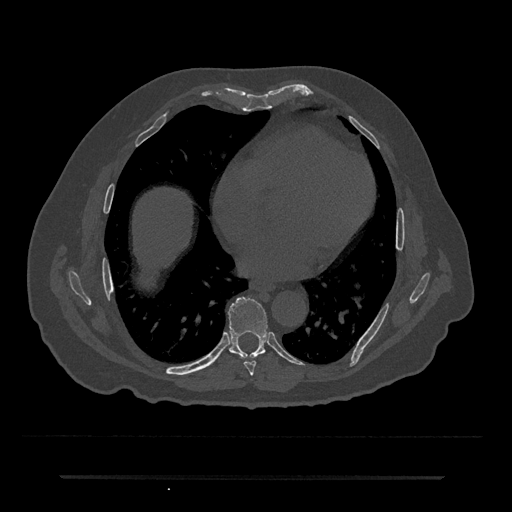
CT including the spine, one axial slice. Slice 355 of 797 in the series (ordered by position). Reconstruction kernel Br40s/3. 120 kVp. Bone window (W 1800 / L 400 HU). 0.5 mm slice thickness. 512 × 512 image matrix, field of view 437 × 437 mm. Patient: male, 69 years. Case-level facts recorded for this patient, not image findings: primary cancer: prostate.
Outlined on this slice (semi-automatic segmentation, software-assisted and operator-edited):
- T7 vertebra: bounding box <244,361,256,376> (left, top, right, bottom; pixels)
- T8 vertebra: <228,297,267,359>